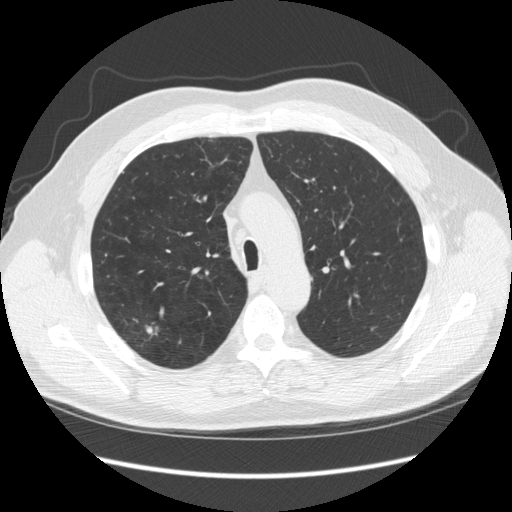
Chest CT (low-dose screening protocol), one axial image, third screening round (two years after baseline), lung window (W 1500 / L -600 HU). Male participant, aged 64 years at enrolment. Former smoker at enrolment.
Expert-annotated lung lesion, bounding box <117,314,171,358> (left, top, right, bottom; pixels). The screening reader recorded 4 non-calcified nodules or masses ≥4 mm on this exam (right upper lobe, right upper lobe, right upper lobe, right upper lobe); which of them this box marks is not recorded. Official screen result: positive, other. Lung cancer was diagnosed 15 days after this screen: adenocarcinoma, NOS, right upper lobe, moderately differentiated (G2), stage IA (AJCC 6th edition), 14 mm at pathology.